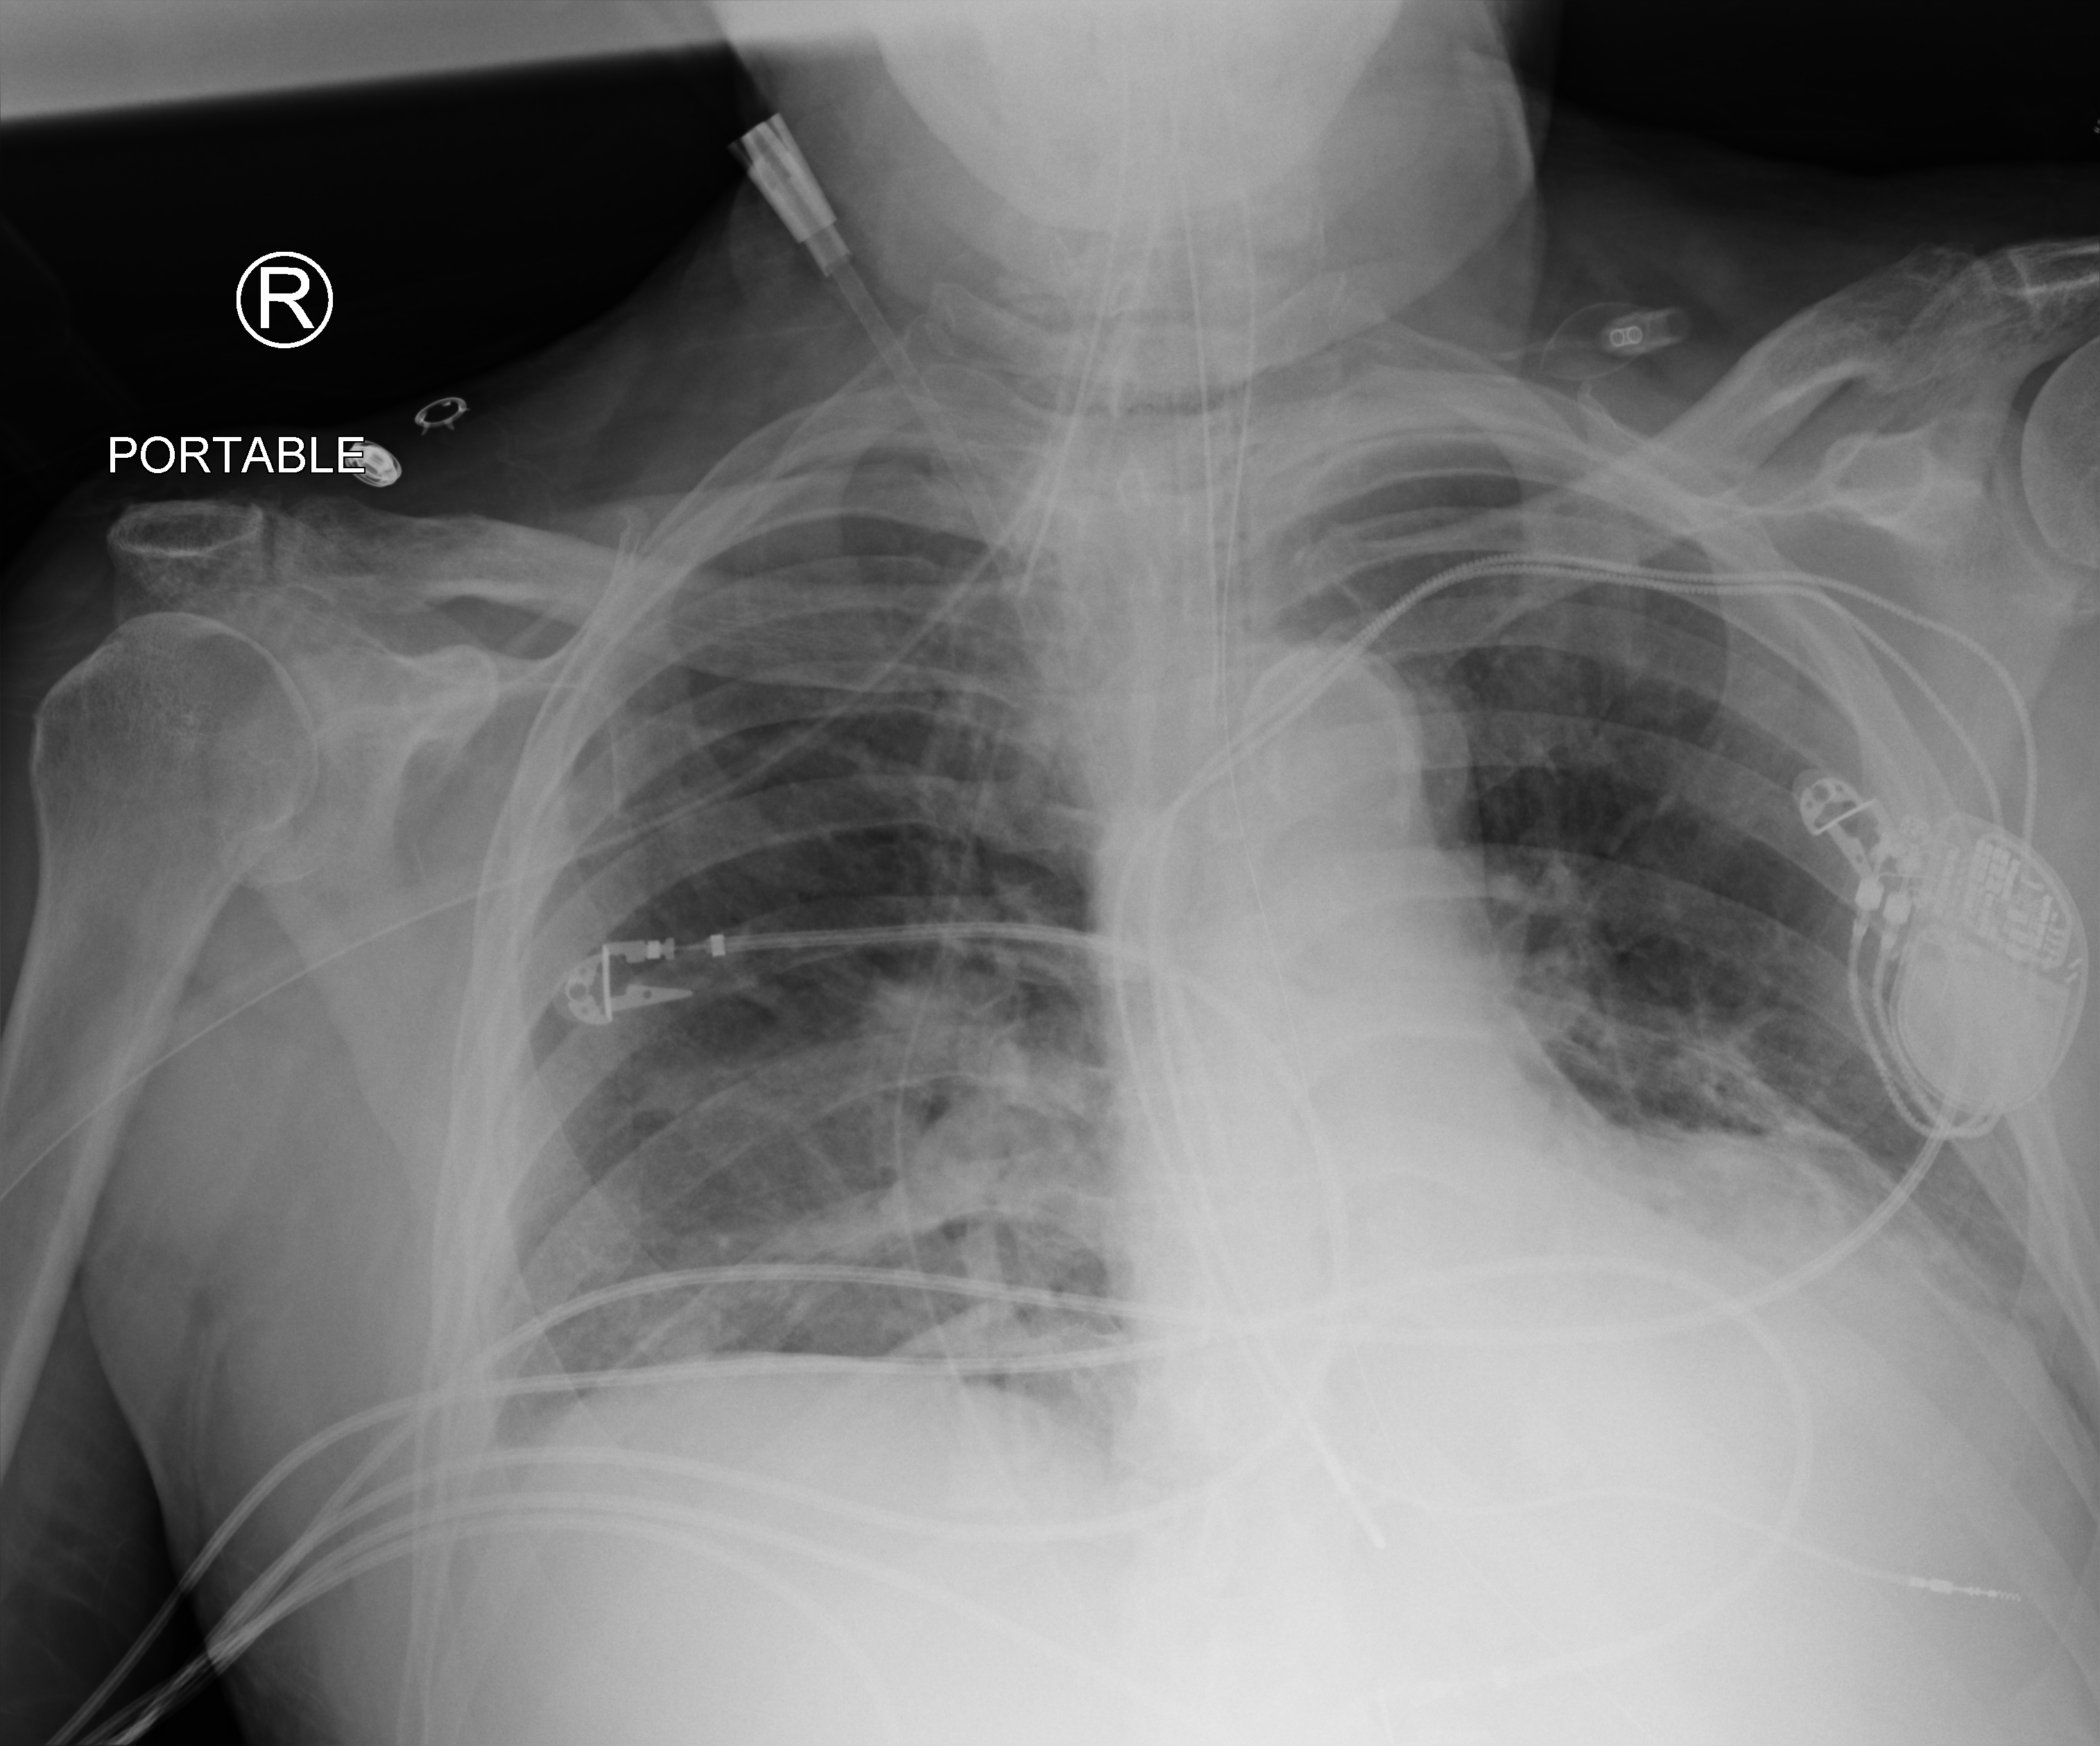
Bedside chest radiograph (computed radiography); anteroposterior (AP) projection. Male patient hospitalised with COVID-19, age 60–74 years.
Admission-level facts for this patient (not findings on this image; timing relative to this image not recorded): admitted to intensive care during this hospital stay: yes.